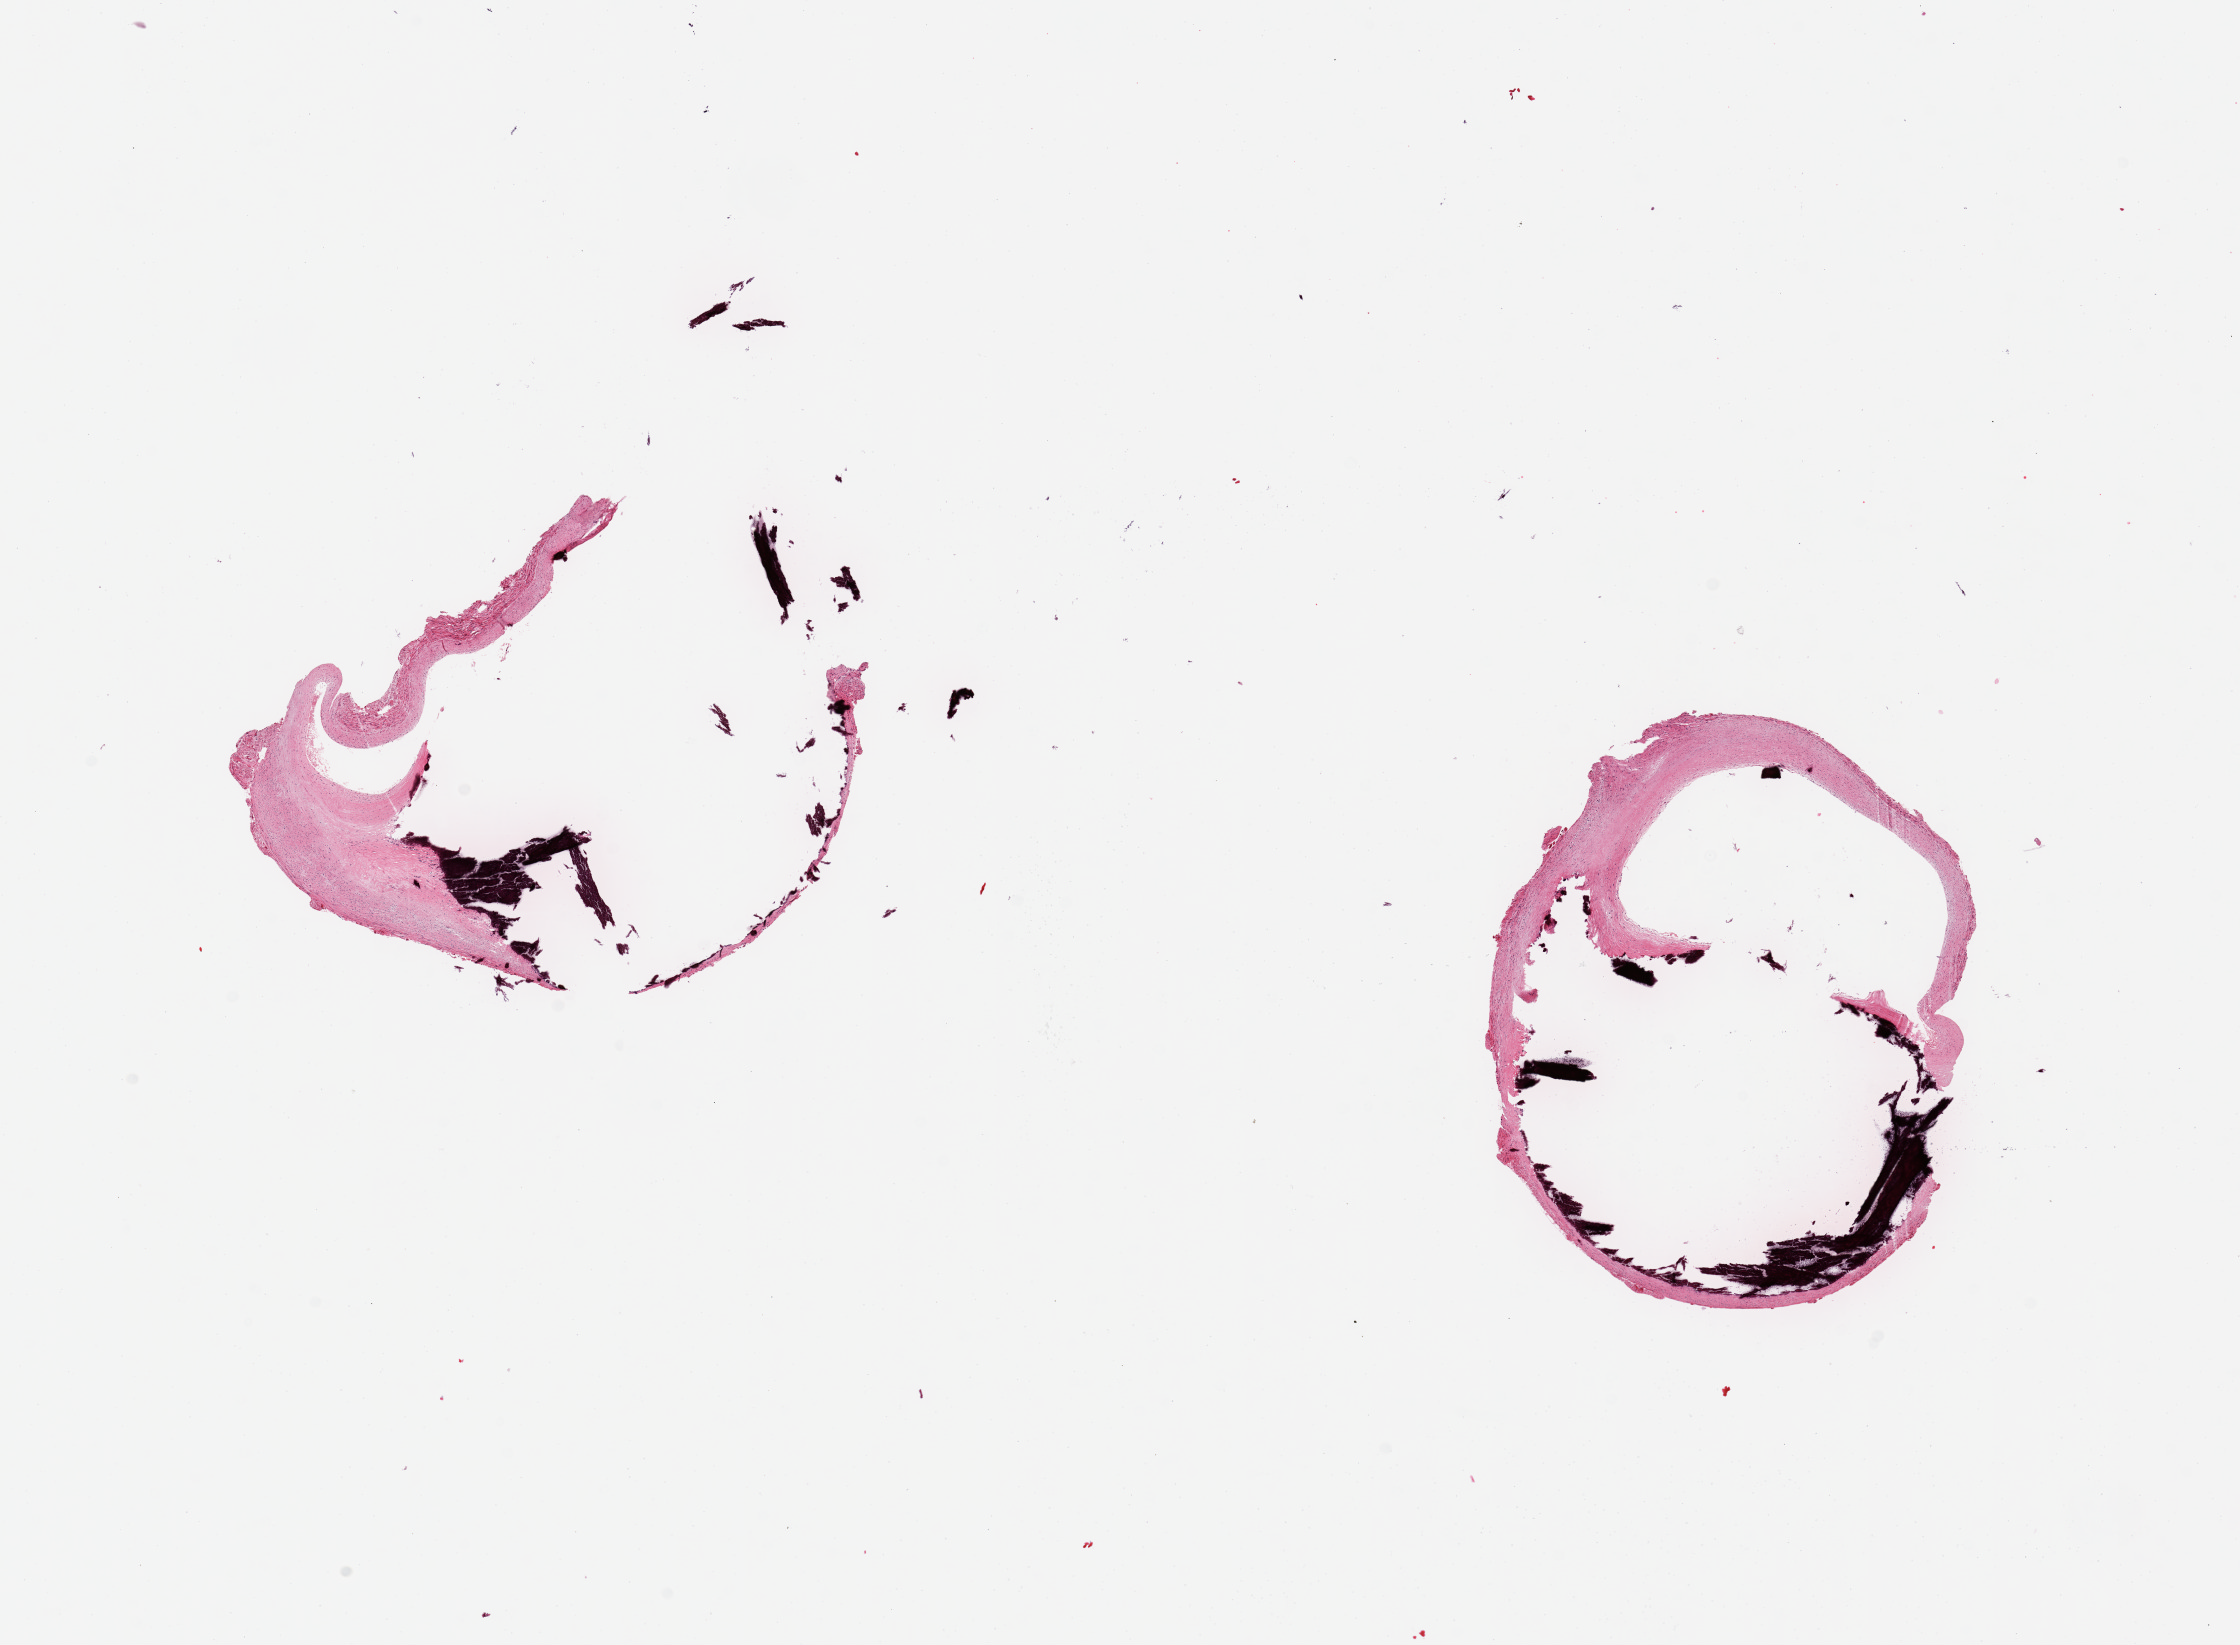
Digitized haematoxylin and eosin-stained section — low-resolution overview of the scanned area, about 17.7 x 13.0 mm; PAXgene-fixed, paraffin-embedded tissue; target tissue: coronary artery; tissue donor sample.
Reviewer comment on this tissue sample: 2 pieces; one fragmented.